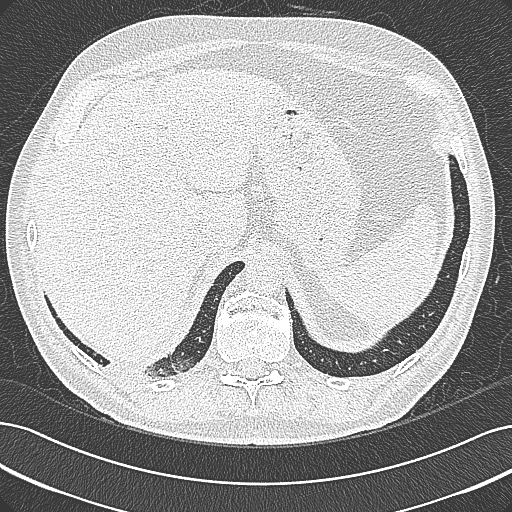
Chest CT (low-dose screening protocol), one axial image; baseline screening round; lung window (W 1500 / L -600 HU); 1 mm slice thickness; slice 267 of 355 in the series; 512 × 512 image matrix. Male, age 68 years at enrolment. Former smoker at enrolment.
Expert-annotated lung lesion, box from (x=92, y=335) to (x=198, y=395) px. Screening reader's record for this exam: no non-calcified nodule ≥4 mm recorded. Later outcome: lung cancer diagnosed 154 days after this screen — mucinous adenocarcinoma, right lower lobe, well differentiated (G1), stage IB (AJCC 6th edition), 50 mm at pathology.